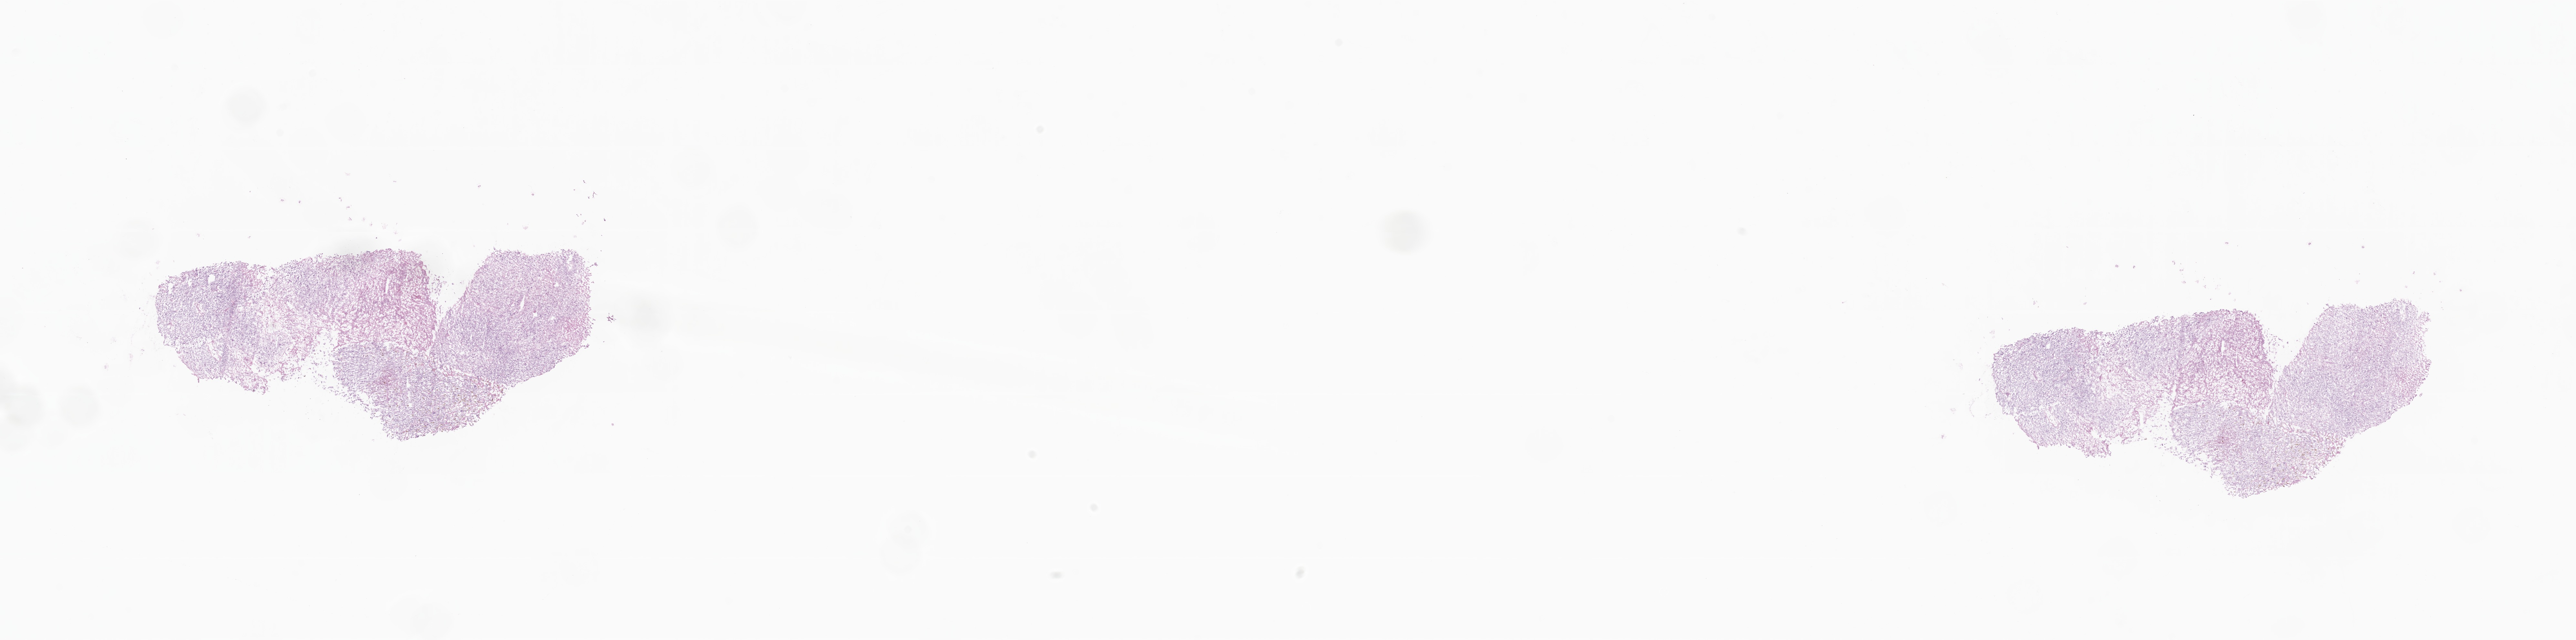
Whole-slide image, H&E stain, low-resolution overview of the scanned area, about 33.6 x 8.4 mm. Cryosection. Specimen: metastatic tumor tissue. Female, age 67 years at initial diagnosis. Slide review estimates, as recorded: tumor cells 56%, tumor nuclei 80%.
Patient diagnosis (primary): Giant cell sarcoma.